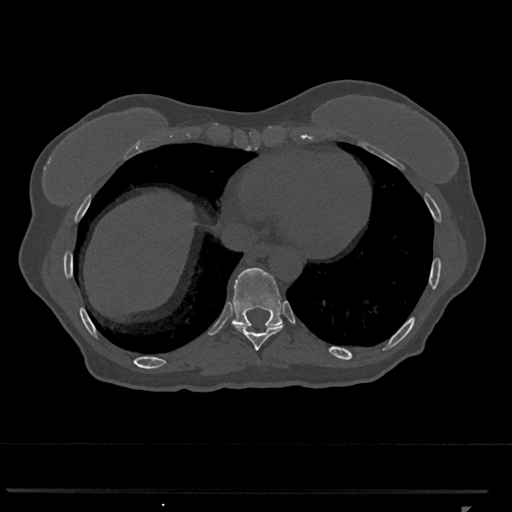
CT including the spine, one axial slice; bone window (W 1800 / L 400 HU); 0.5 mm slice thickness; 512 × 512 image matrix, field of view 380 × 380 mm. Female patient, age 62 years. Case-level facts recorded for this patient, not image findings: primary cancer: renal.
Outlined on this slice (semi-automatic segmentation, software-assisted and operator-edited):
- T10 vertebra: bounding box (x1, y1, x2, y2) in pixels: (231, 267, 283, 327)
- T9 vertebra: (233, 323, 283, 351)